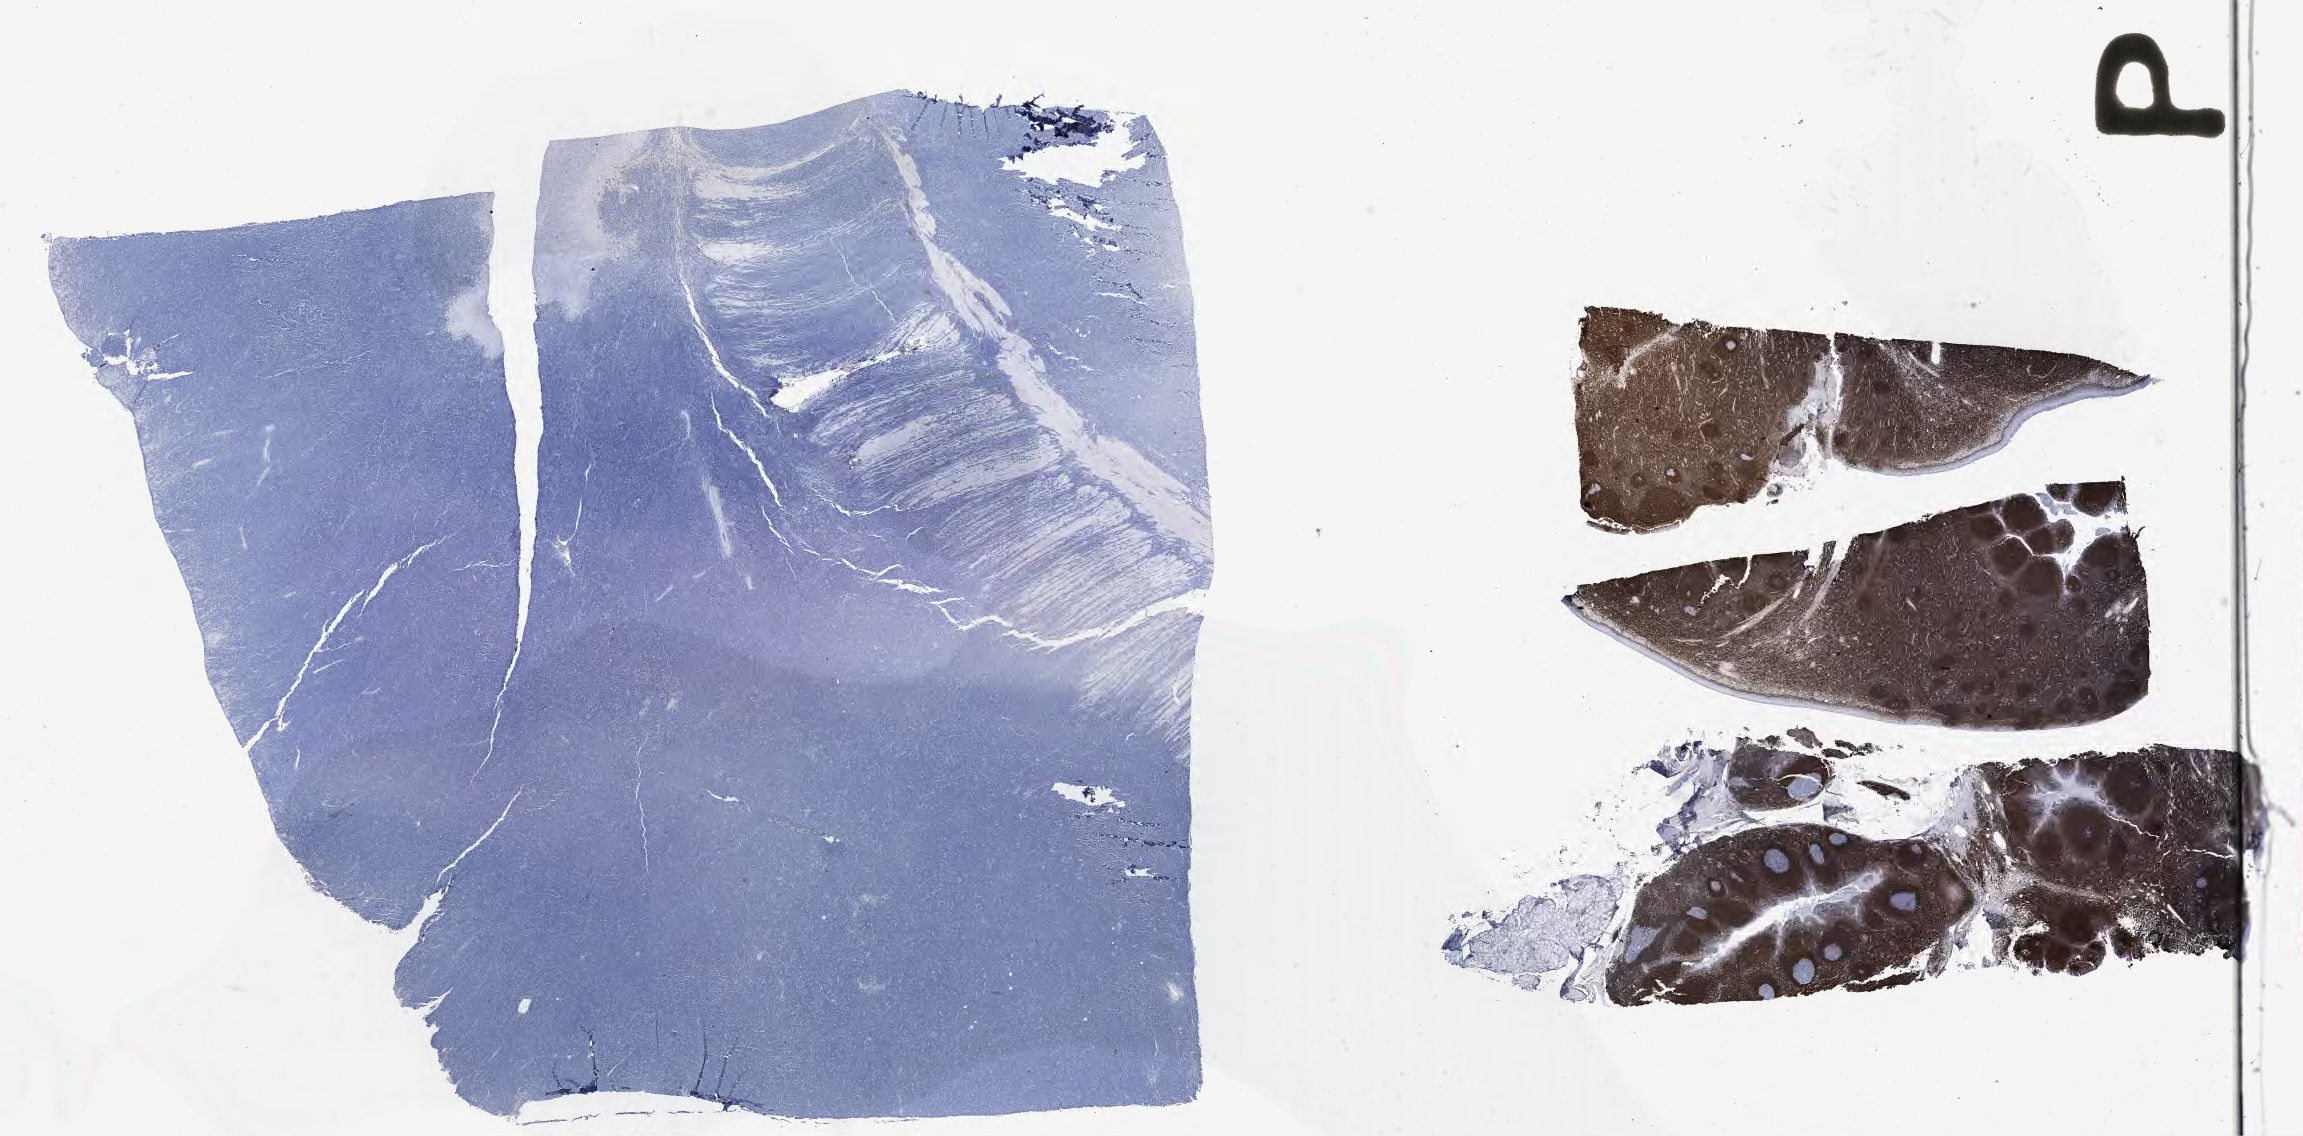
Immunohistochemistry (IHC) whole-slide image stained for BCL2 — shown as a low-resolution overview of the whole scanned area (about 37.2 x 18.4 mm), tumor tissue, anatomic site: colon. Patient male; 14 years old.
Diagnosis: Burkitt lymphoma, NOS.